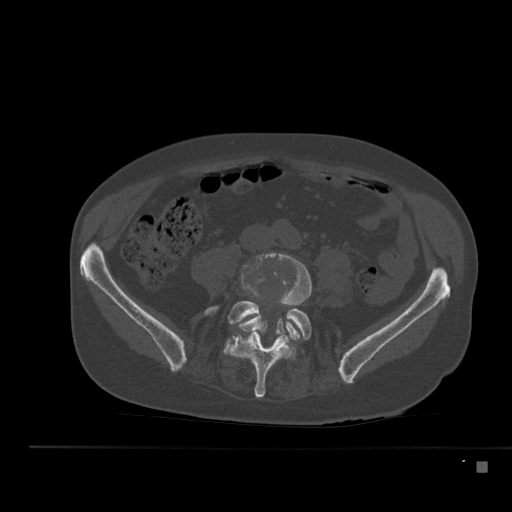
CT including the spine, one axial slice. Slice 132 of 517 in the series (ordered by position). 120 kVp. Bone window (W 1800 / L 400 HU). 512 × 512 image matrix, field of view 408 × 408 mm. Patient: male, 70 years. From the clinical record (not read from this slice): primary cancer: renal.
Structures marked on this image (semi-automatically segmented with operator editing):
- L4 vertebra: bounding box [x1, y1, x2, y2] px = [239, 252, 312, 341]
- L5 vertebra: [205, 301, 312, 398]